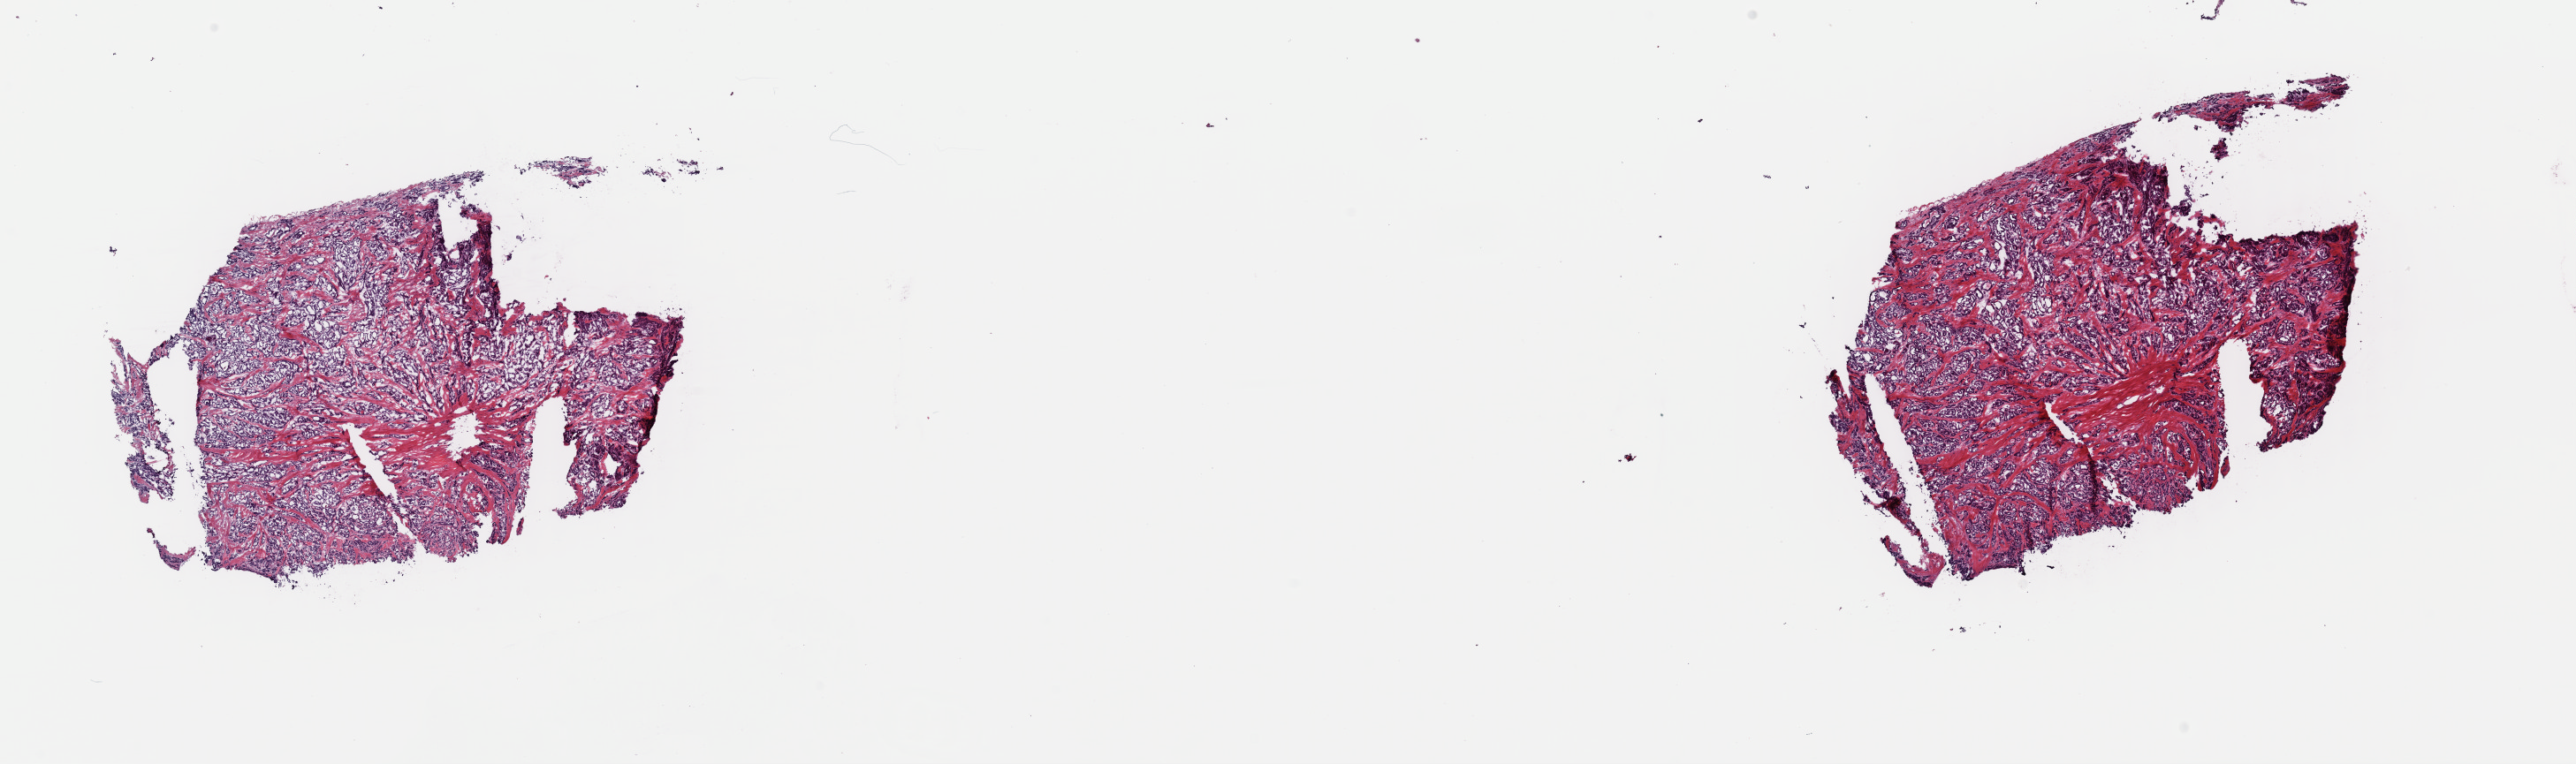
H&E whole-slide image — low-resolution overview of the scanned area, about 23.0 x 6.8 mm (slide scanned at 40x), frozen section from the top of the tissue portion, sample: primary tumour, thyroid. Female, age 50 years at initial diagnosis. Pathologist review of this section (percent, as recorded): tumour cells 100%, tumour nuclei 90%, normal cells 0%, stromal cells 0%, necrosis 0%. Inflammatory infiltration, as recorded: lymphocyte infiltration 0%, monocyte infiltration 0%, neutrophil infiltration 0%.
Diagnosis: Papillary carcinoma, follicular variant (thyroid gland).